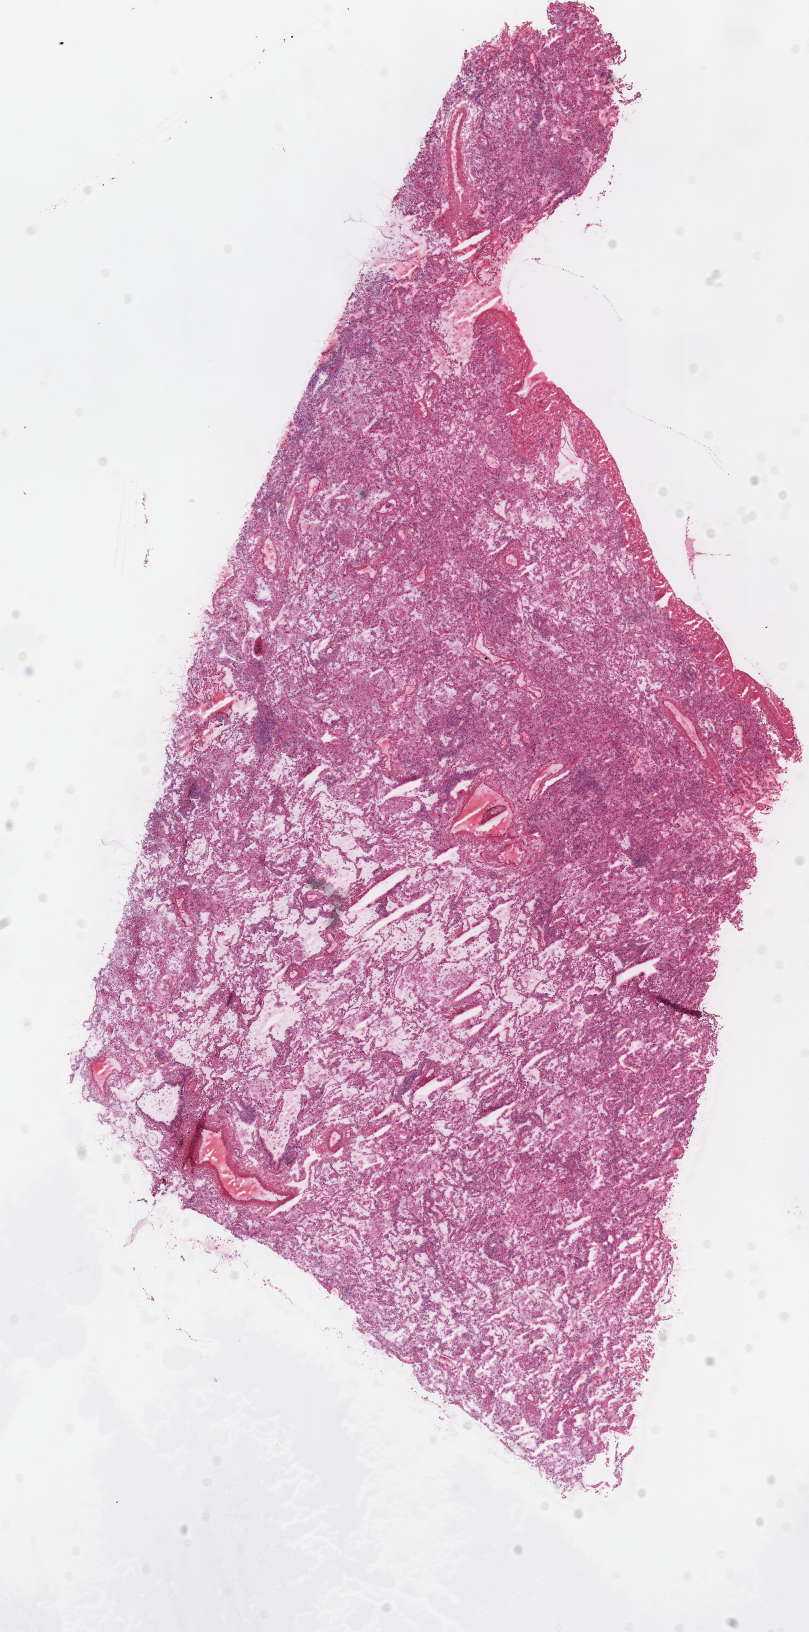
Whole-slide histology image, H&E, a low-resolution overview of the entire scanned area, about 6.4 x 12.8 mm (from a 40x scan). Frozen section from the top of the tissue portion. Lung, solid tissue normal (non-tumour tissue) sample. Female, age 69 years at initial diagnosis. Inflammatory infiltration, as recorded: lymphocyte infiltration 10%, monocyte infiltration 30%, neutrophil infiltration 0%.
* this section: solid tissue normal (non-tumour) sample from the same patient
* patient diagnosis: Adenocarcinoma with mixed subtypes